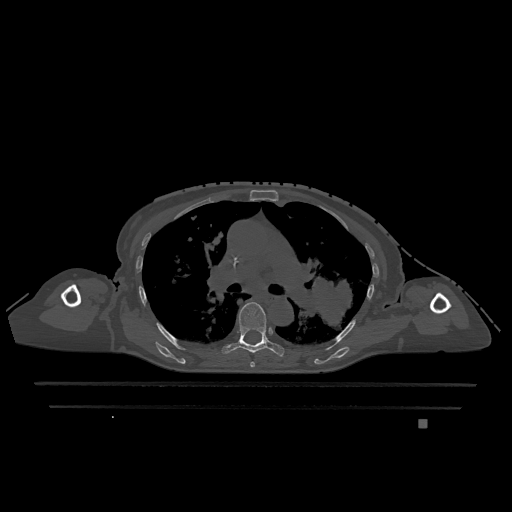
CT including the spine, one axial slice. Position 793 of 1317 along the scan axis. Bone window (W 1800 / L 400 HU). 0.5 mm slice thickness. 512 × 512 image matrix, field of view 500 × 500 mm. Female patient, age 74 years. Case-level facts recorded for this patient, not image findings: primary cancer: lung; vertebrae with lytic lesions (as recorded): T1, T4, T5, T6, L4, L5.
Annotated regions visible in this slice (semi-automatically segmented with operator editing):
- T5 vertebra: box from (x=250, y=361) to (x=255, y=368) px
- T6 vertebra: (x=222, y=302)–(x=285, y=357)